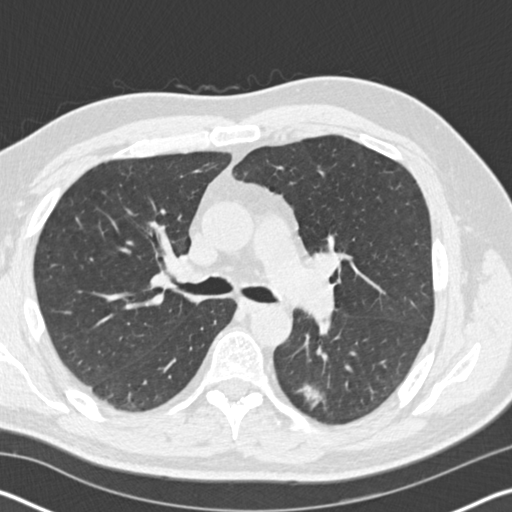
Low-dose screening chest CT, one axial slice. Slice 107 of 178 in the series (ordered by position). Reconstruction kernel B30f. 120 kVp. Lung window (W 1500 / L -600 HU). 512 × 512 image matrix, field of view 340 × 340 mm.
Outlined on this slice (outlined manually by an expert reader):
- lesion 1 (tumor, lower lobe of left lung): box from (x=298, y=384) to (x=324, y=408) px